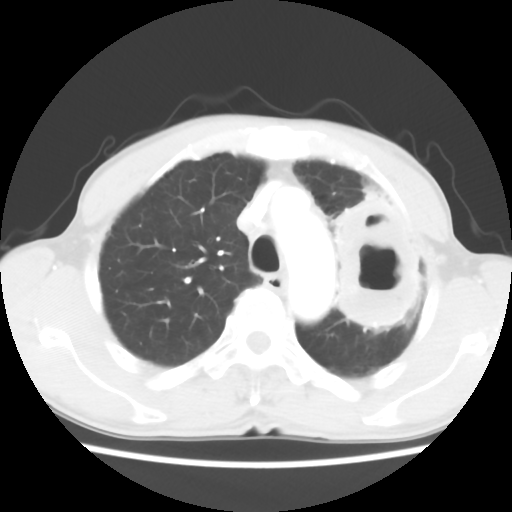
Chest CT, one axial slice; position 45 of 60 along the scan axis; reconstruction kernel STANDARD; 120 kVp; lung window (W 1500 / L -600 HU); 5 mm slice thickness; 512 × 512 image matrix. Male patient, age 64 years. From the clinical record (not read from this slice): clinical TNM (as recorded): T3 N3 M0; histopathological grade: G3.
Outlined on this slice (rectangle marked by the reading radiologist):
- lung tumour (recorded histology: adenocarcinoma): bounding box (x1, y1, x2, y2) in pixels: (320, 179, 421, 342)